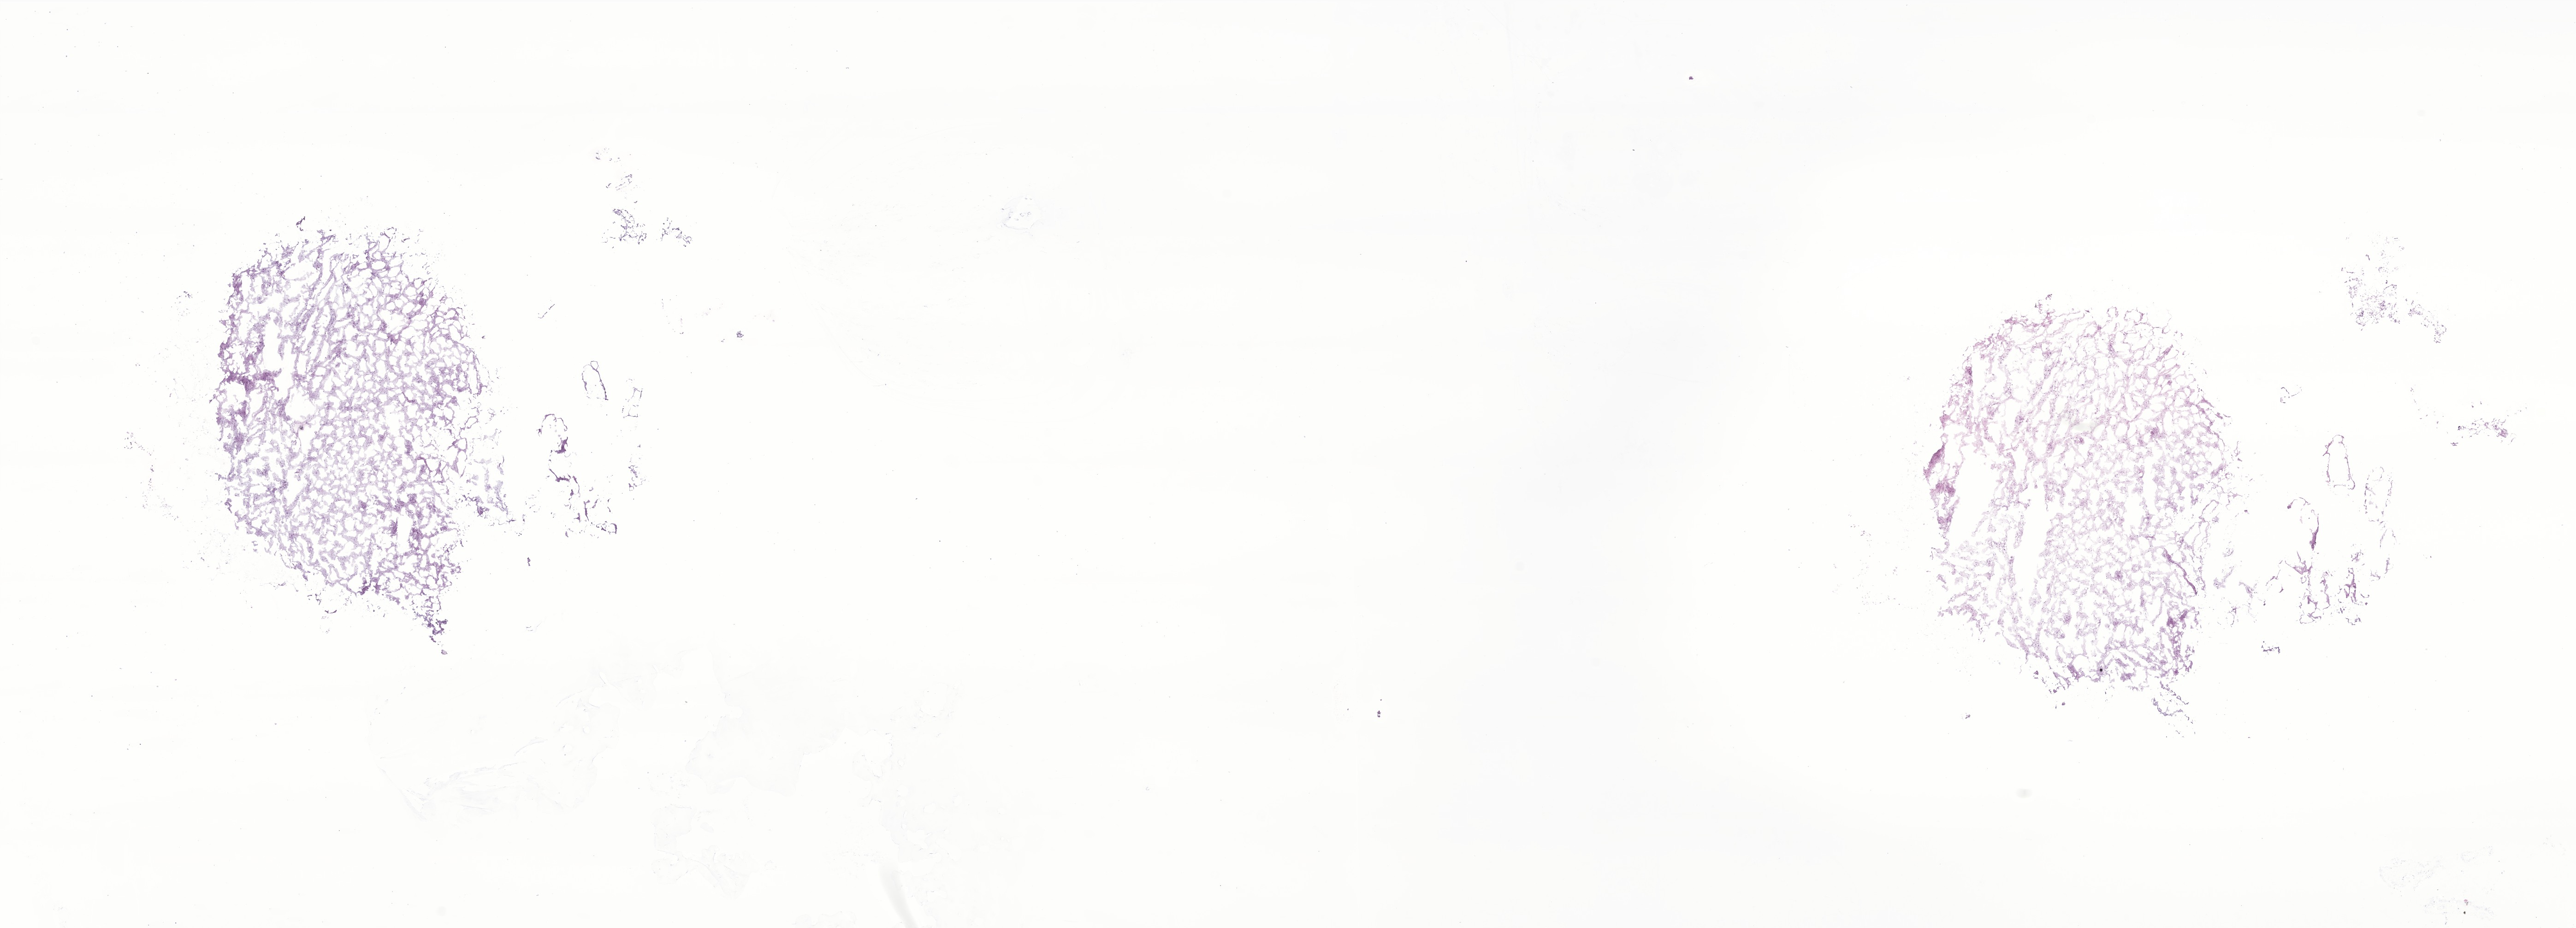
Haematoxylin and eosin whole-slide image of tumor tissue from the frontal lobe — a low-resolution overview of the entire scanned area, about 23.6 x 8.5 mm. Frozen section. Patient male; age 198 months (16 years 6 months).
* recorded diagnosis: Oligoastrocytoma, NOS